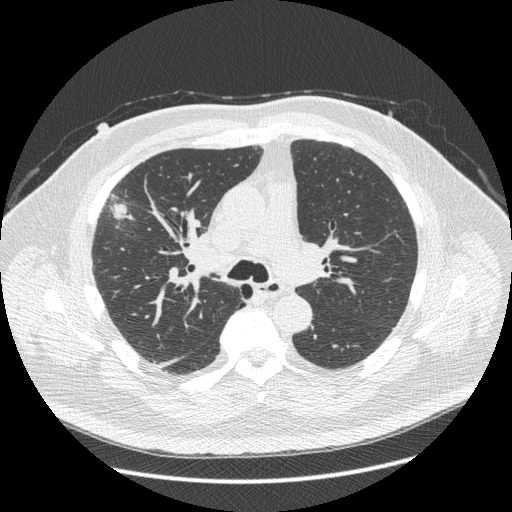
Axial slice from a low-dose chest CT screening exam. Third screening round (two years after baseline). Lung window (W 1500 / L -600 HU). 1.25 mm slice thickness. Slice 156 of 426 in the series. Male, age 66 years at enrolment.
Expert reader's lesion annotation, bounding box (x1, y1, x2, y2) in pixels: (86, 177, 145, 263). Screening reader's record for this exam (one nodule recorded; not confirmed to be the boxed lesion): non-calcified nodule or mass ≥4 mm, right upper lobe, 48 × 25 mm, spiculated (stellate) margins, soft tissue attenuation, pre-existing on the prior screen: no. Lung cancer was diagnosed 35 days after this screen: non-small cell carcinoma, right upper lobe, stage IV (AJCC 6th edition), 50 mm at pathology.